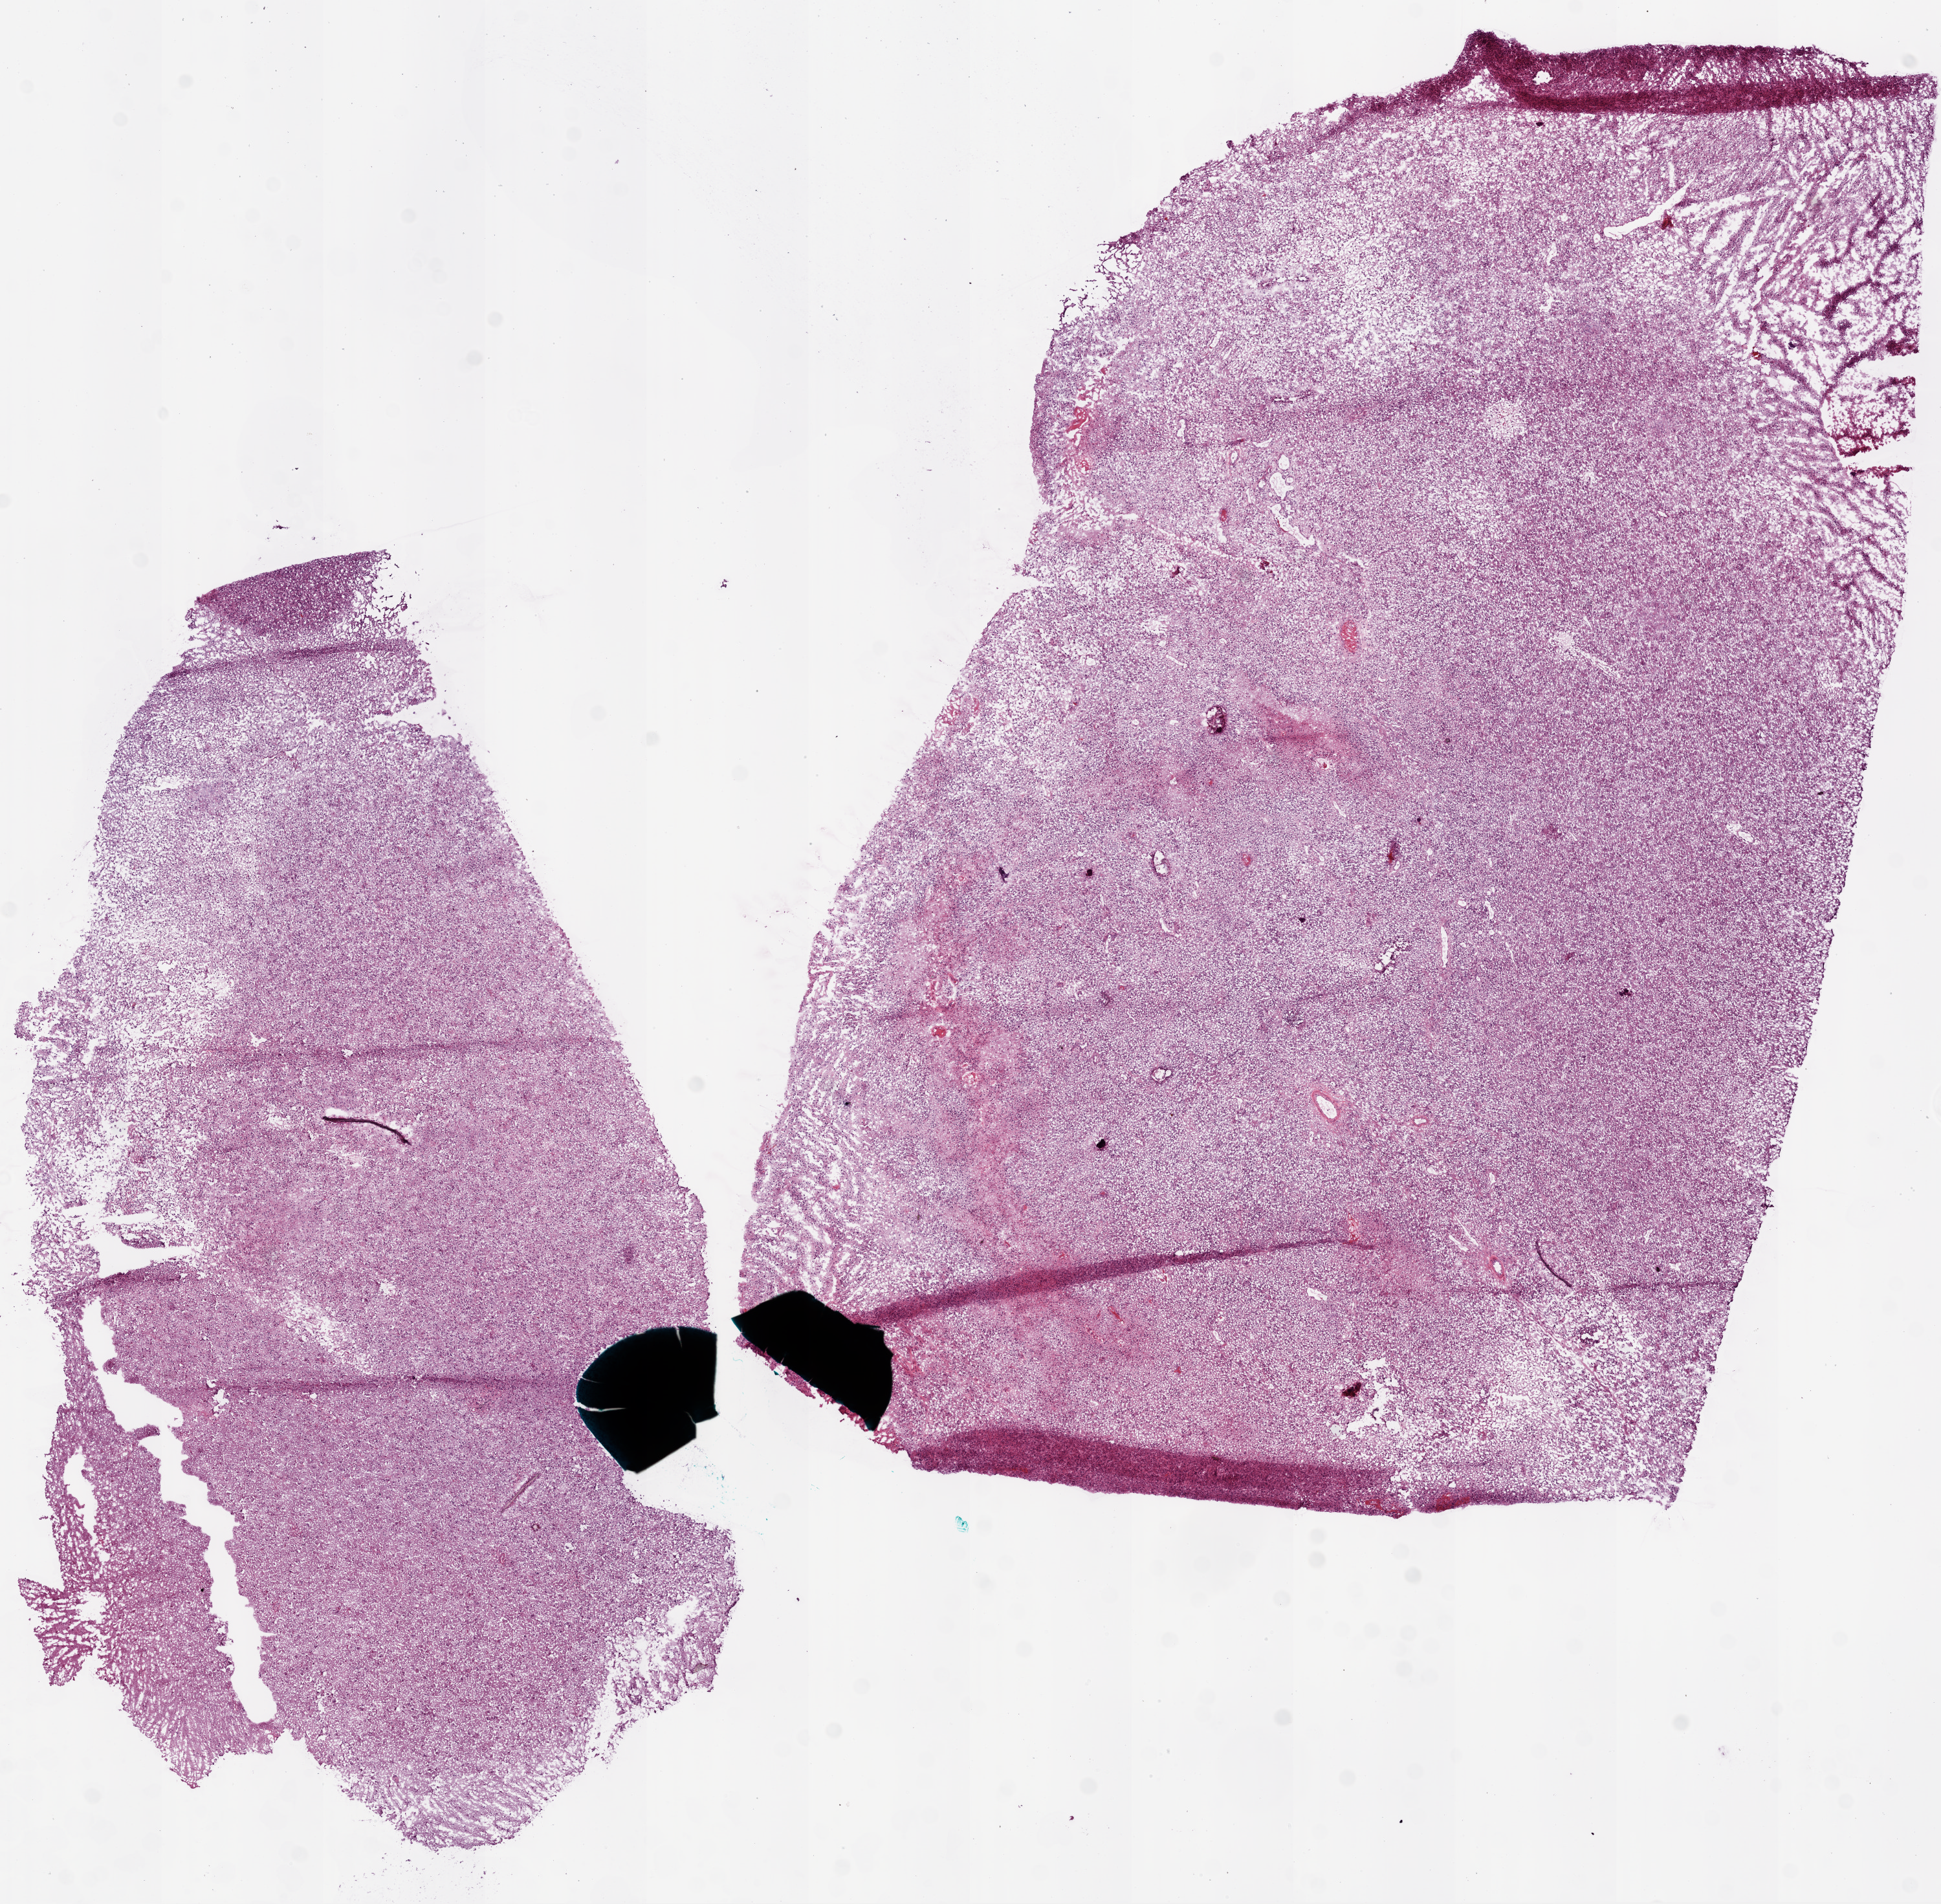
Hematoxylin and eosin (H&E) stained whole-slide image — whole scanned area (about 12.0 x 11.8 mm, acquisition: 20x scan) shown as a low-resolution overview; frozen section from the bottom of the tissue portion; primary tumour sample from the brain. Patient: male, age at initial diagnosis 48 years. Pathologist review of this section (percent, as recorded): tumour cells 85%, tumour nuclei 90%, normal cells 5%, stromal cells 5%, necrosis 5%.
• histologic diagnosis: Glioblastoma